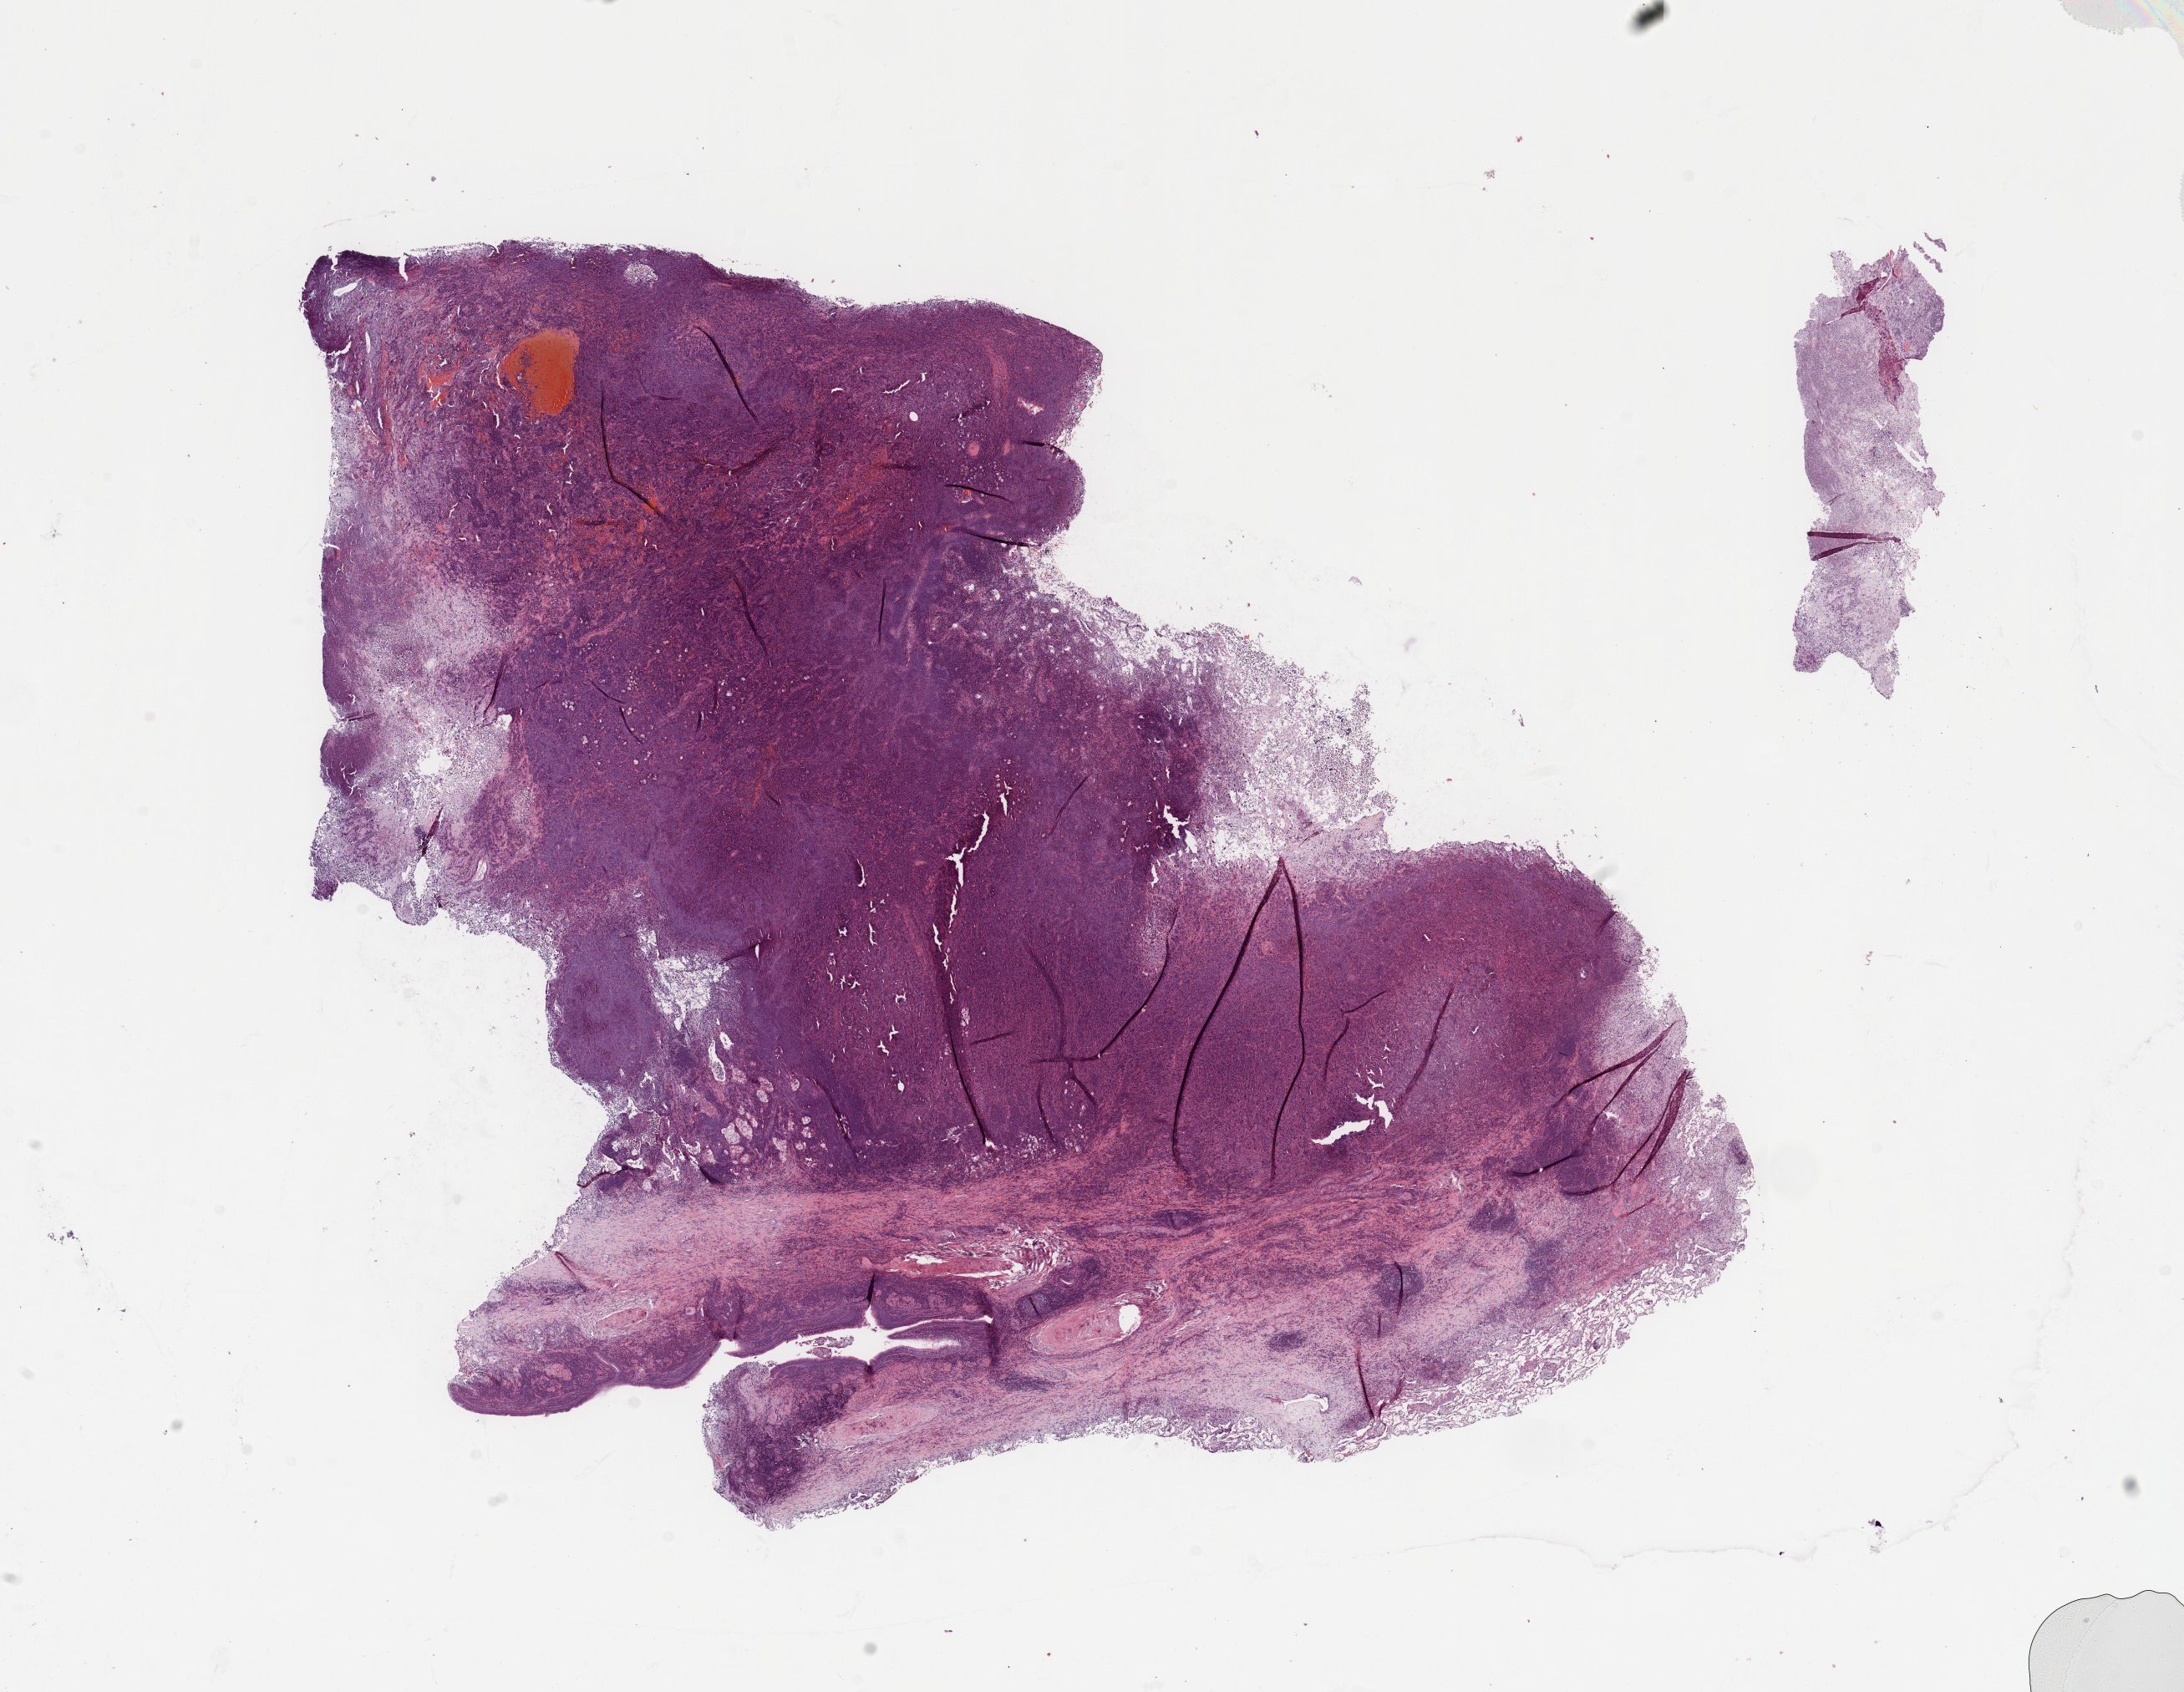
Digitized Hematoxylin and eosin (H&E) stained tissue section (whole slide) — a low-resolution overview of the entire scanned area, about 20.7 x 16.0 mm (slide scanned at 20x), tumour tissue sample, sampled site: lung. 70-year-old female patient. Histologic grade: G3 (poorly differentiated). Composition of this section per pathologist review: tumour nuclei 75%, necrosis 5%.
Diagnosis: Squamous cell carcinoma, NOS. Primary tumour site (as recorded): right lower lobe.